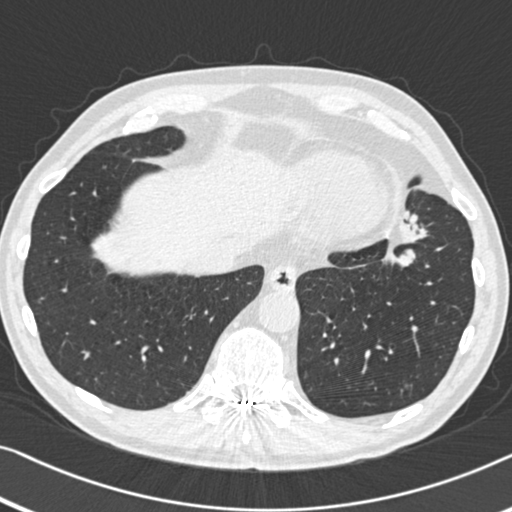
Low-dose screening chest CT, one axial slice; position 121 of 383 along the scan axis; 120 kVp; lung window (W 1500 / L -600 HU); 512 × 512 image matrix.
Structures marked on this image (expert manual segmentation):
- lesion 1 (tumor, upper lobe of left lung): bounding box [x1, y1, x2, y2] px = [384, 213, 427, 267]